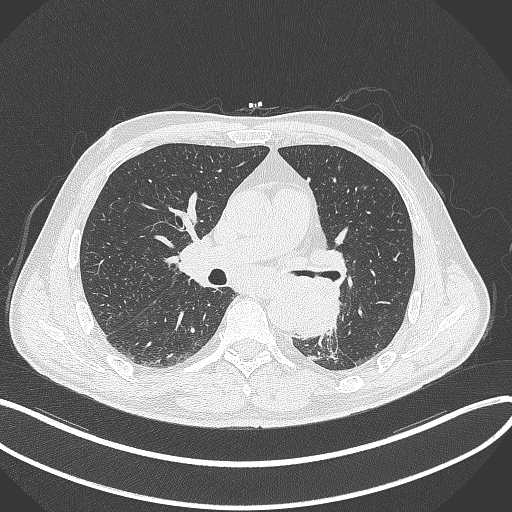
Chest CT, one axial slice. Slice 190 of 329 in the series (ordered by position). Reconstruction kernel B70f. 120 kVp. Lung window (W 1500 / L -600 HU). 1 mm slice thickness. 512 × 512 image matrix. Male patient, age 59 years. Case-level facts recorded for this patient, not image findings: clinical TNM (as recorded): T2a N2 M0.
Outlined on this slice (bounding box drawn by a radiologist):
- lung tumour (recorded histology: squamous cell carcinoma): bounding box (x1, y1, x2, y2) in pixels: (296, 278, 348, 344)